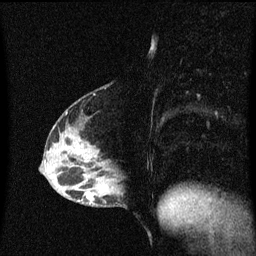
Breast MRI (dynamic contrast-enhanced), one sagittal slice. Position 24 of 60 along the scan axis. Dynamic contrast-enhanced series, image 2 of 3 at this slice position (ordered by acquisition). 1.5 T. TE 4.2 ms, TR 8.4 ms. 2 mm slice thickness. 256 × 256 image matrix, field of view 200 × 200 mm. Patient: female, 40 years.
Annotated regions visible in this slice (semi-automatic segmentation, software-assisted and operator-edited):
- analysis volume of interest (the breast-tissue region the enhancement analysis was run in; not a lesion): bounding box (x1, y1, x2, y2) in pixels: (82, 172, 127, 209)
- tumour enhancement mask (voxels above the 70 % enhancement threshold inside the analysis volume of interest): (87, 194, 95, 205)